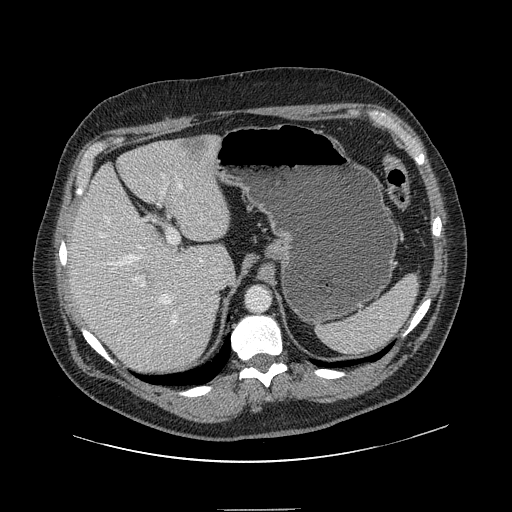
Contrast-enhanced abdominal CT, one axial slice; slice 104 of 154 in the series (ordered by position); 120 kVp; intravenous contrast given; soft-tissue window (W 400 / L 40 HU); 2.5 mm slice thickness; 512 × 512 image matrix, field of view 451 × 451 mm. Male patient, age 61 years. Case-level facts recorded for this patient, not image findings: diagnosis: colorectal cancer liver metastases, imaged before liver resection; multiple liver metastases: yes; largest metastasis: 2.6 cm; disease in both lobes: yes.
Annotated regions visible in this slice (manually delineated by an expert):
- hepatic veins: bounding box <100,182,183,326> (left, top, right, bottom; pixels)
- liver: <68,137,230,375>
- planned liver remnant (the part of the liver to remain after resection): <68,144,230,360>
- portal vein (with intrahepatic branches): <134,174,180,286>
- liver metastasis: <184,139,207,163>